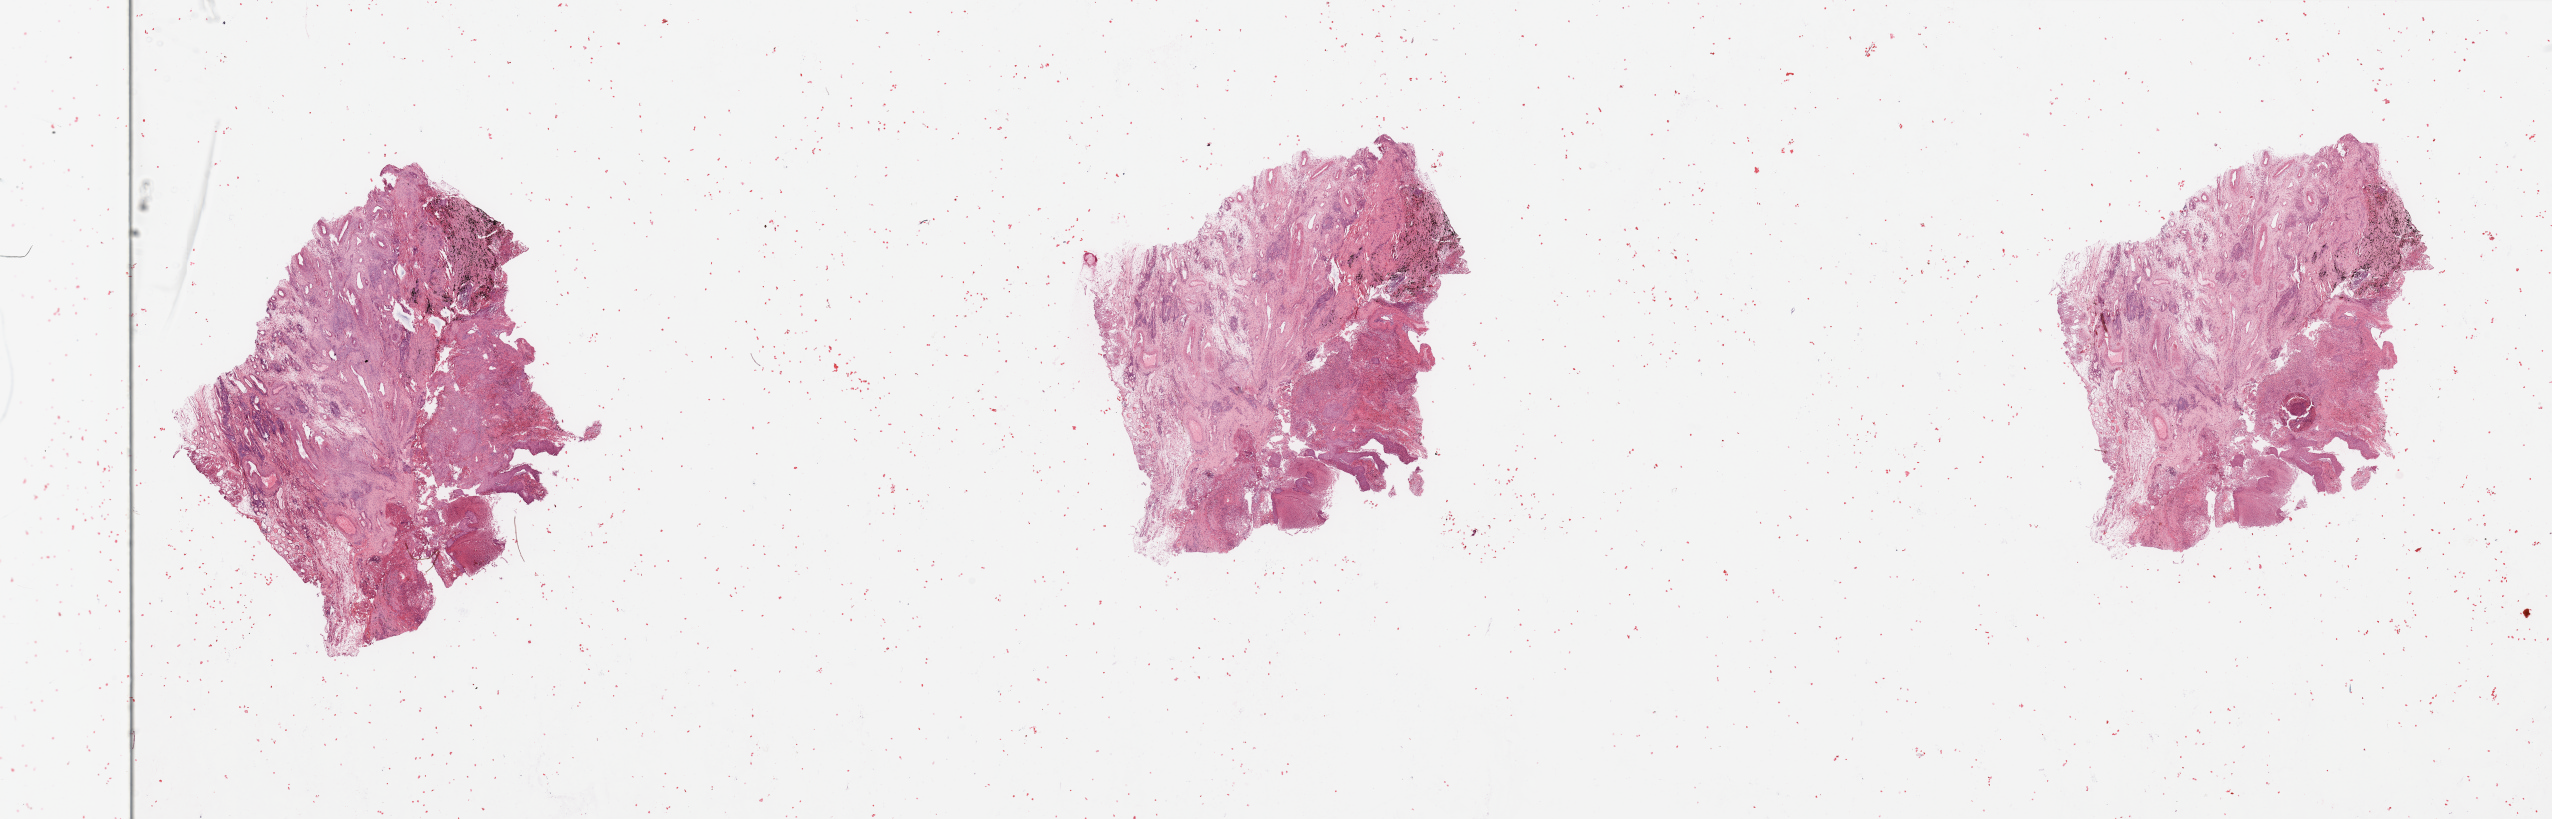
Whole-slide histology image, Hematoxylin and eosin (H&E) stained, a low-resolution overview of the entire scanned area, about 40.4 x 13.0 mm; tumour tissue sample, lung. Patient: male, age 77 years. Histologic grade: G2 (moderately differentiated).
Histologic diagnosis: Squamous cell carcinoma, NOS. Primary tumour site (as recorded): right upper lobe. AJCC pathologic stage: IIB.